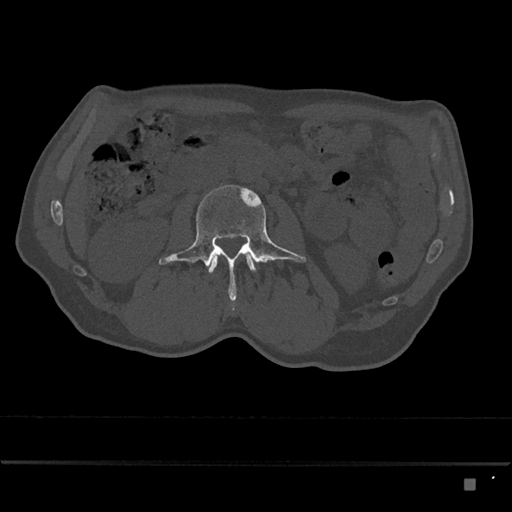
CT including the spine, one axial slice. Slice 421 of 797 in the series (ordered by position). 120 kVp. Bone window (W 1800 / L 400 HU). 0.5 mm slice thickness. 512 × 512 image matrix, field of view 390 × 390 mm. Male patient, age 72 years. From the clinical record (not read from this slice): primary cancer: prostate.
Annotated regions visible in this slice (semi-automatic segmentation, software-assisted and operator-edited):
- L2 vertebra: box from (x=208, y=254) to (x=256, y=273) px
- L3 vertebra: (x=159, y=185)–(x=306, y=301)